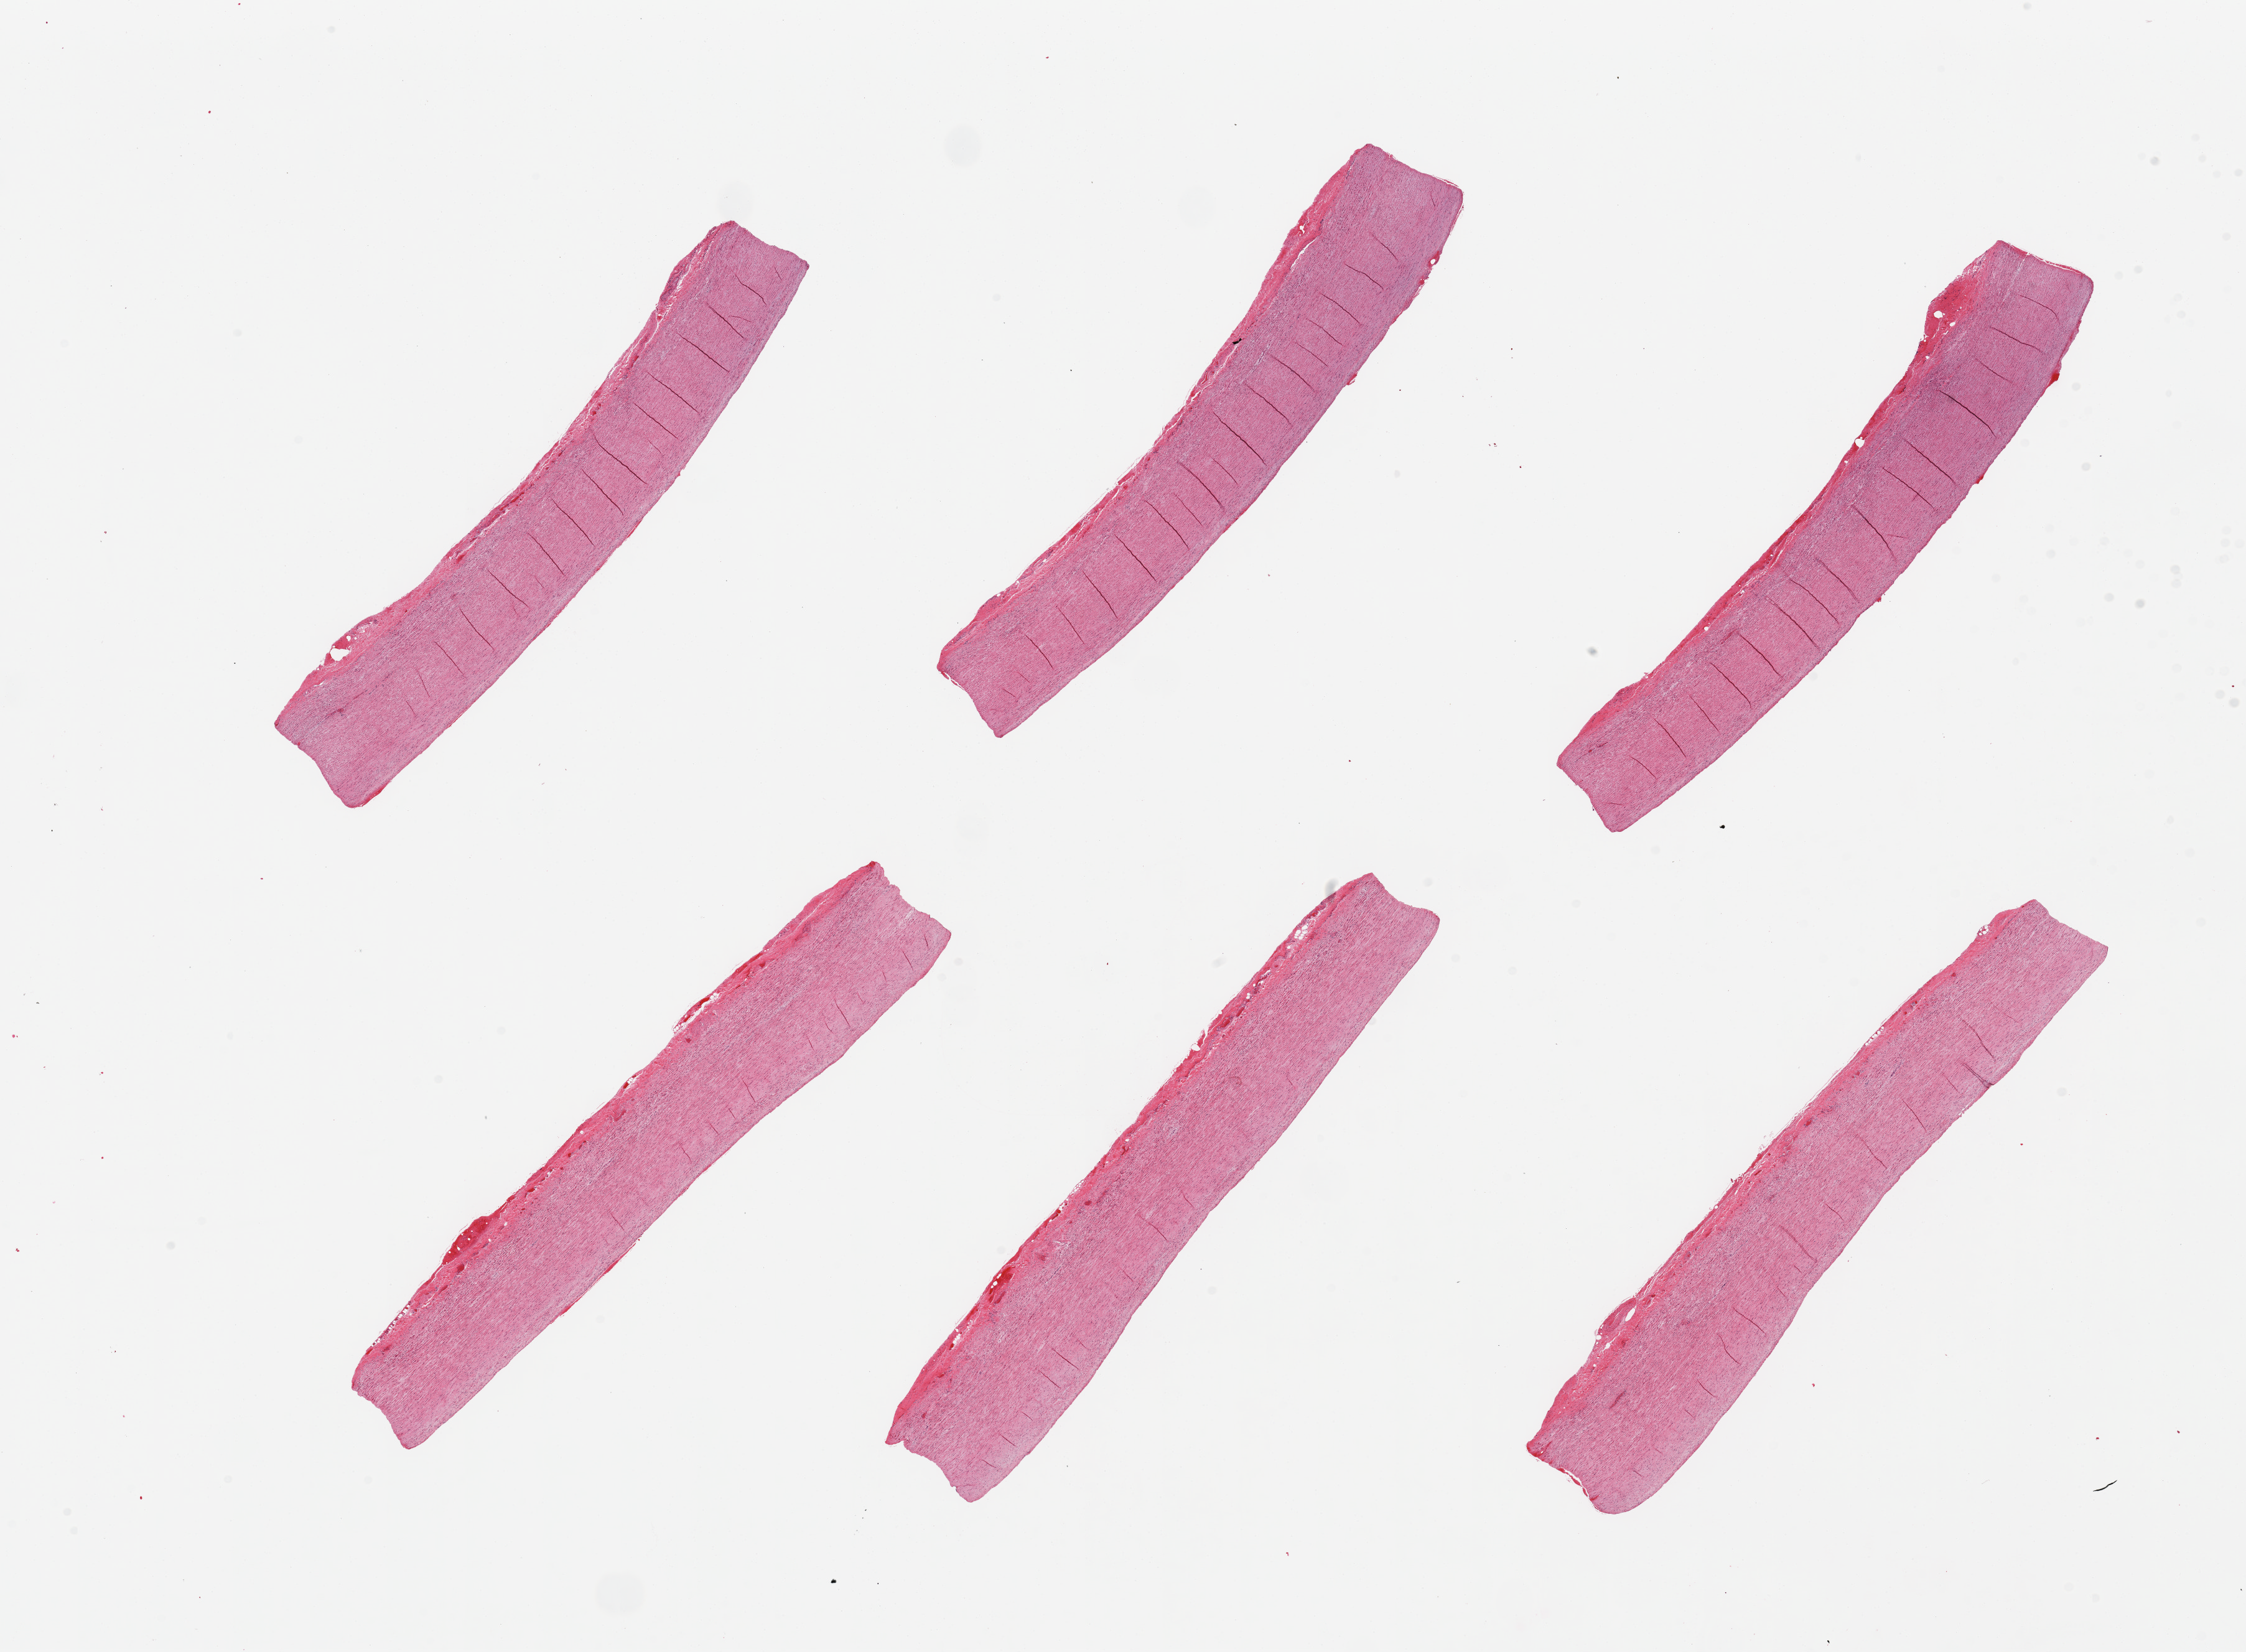
Whole-slide image, H&E stain, brightfield, low-resolution overview of the scanned area, about 28.5 x 21.0 mm, PAXgene-fixed paraffin-embedded (PFPE) section, section of aorta (target tissue), donor tissue sample. Male donor.
• review note (as recorded): 6 pieces, minimal atherosis